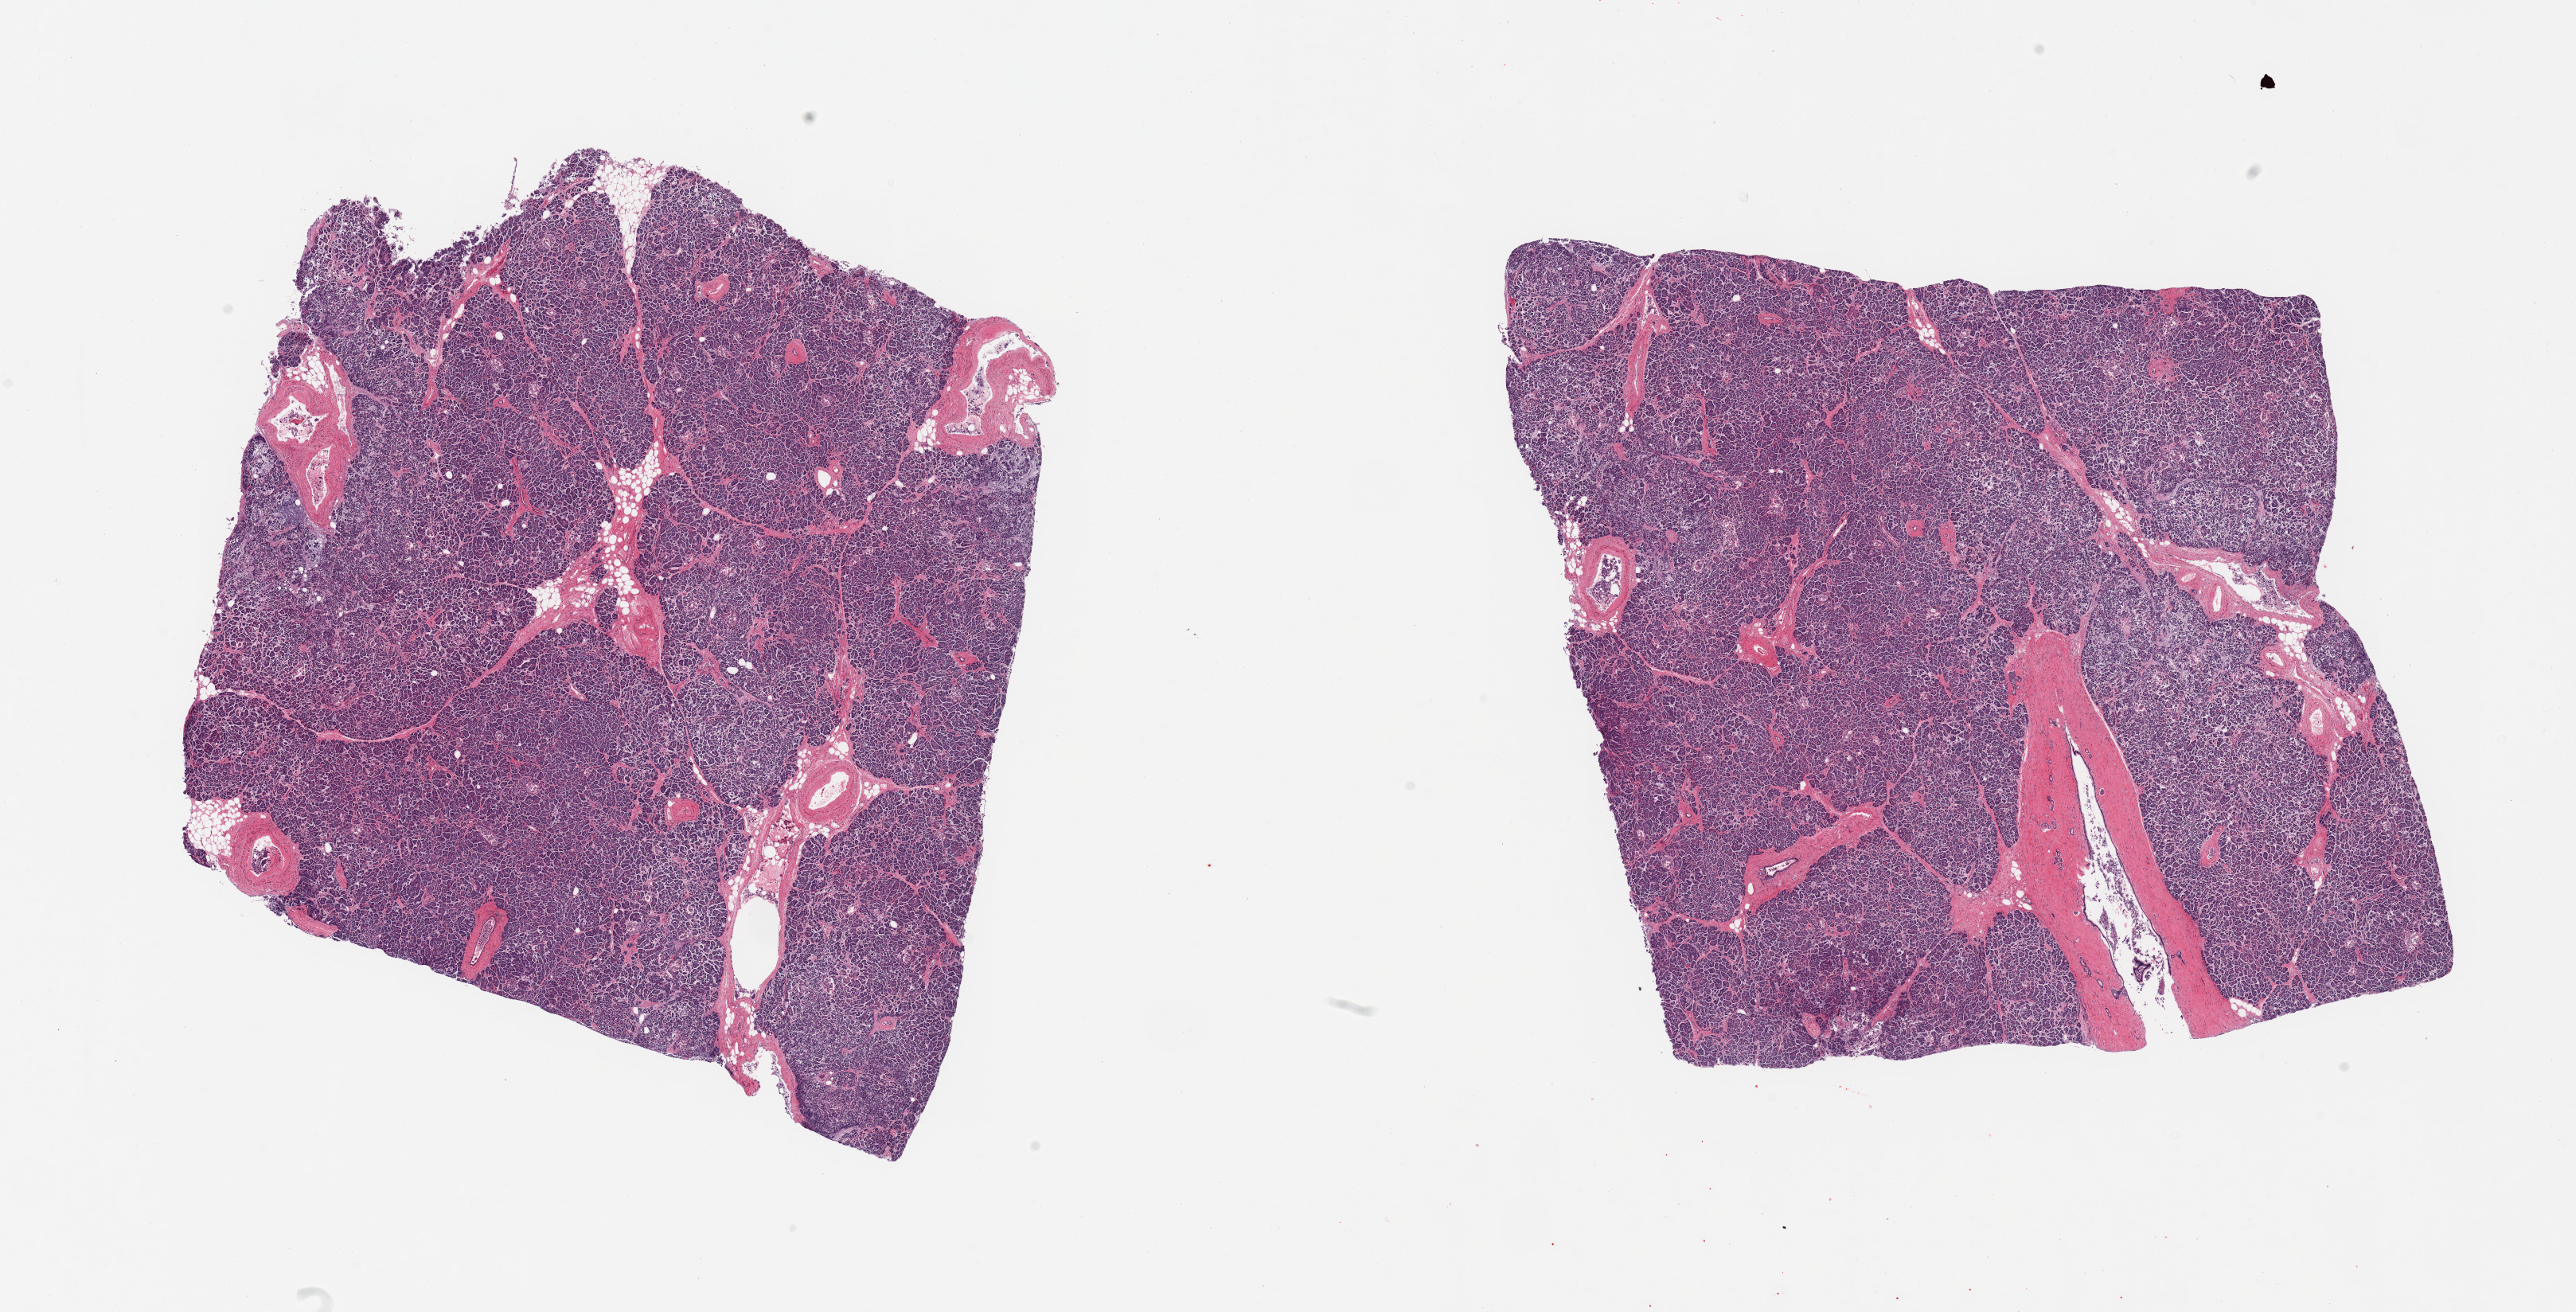
Digitized haematoxylin and eosin-stained section, brightfield, a low-resolution overview of the entire scanned area, about 25.6 x 13.0 mm; PAXgene-fixed paraffin-embedded (PFPE) section; target tissue: pancreas; tissue donor sample. Donor: male.
Reviewer comment on this tissue sample: 2 pieces, Islets still visible, but disentegrating.